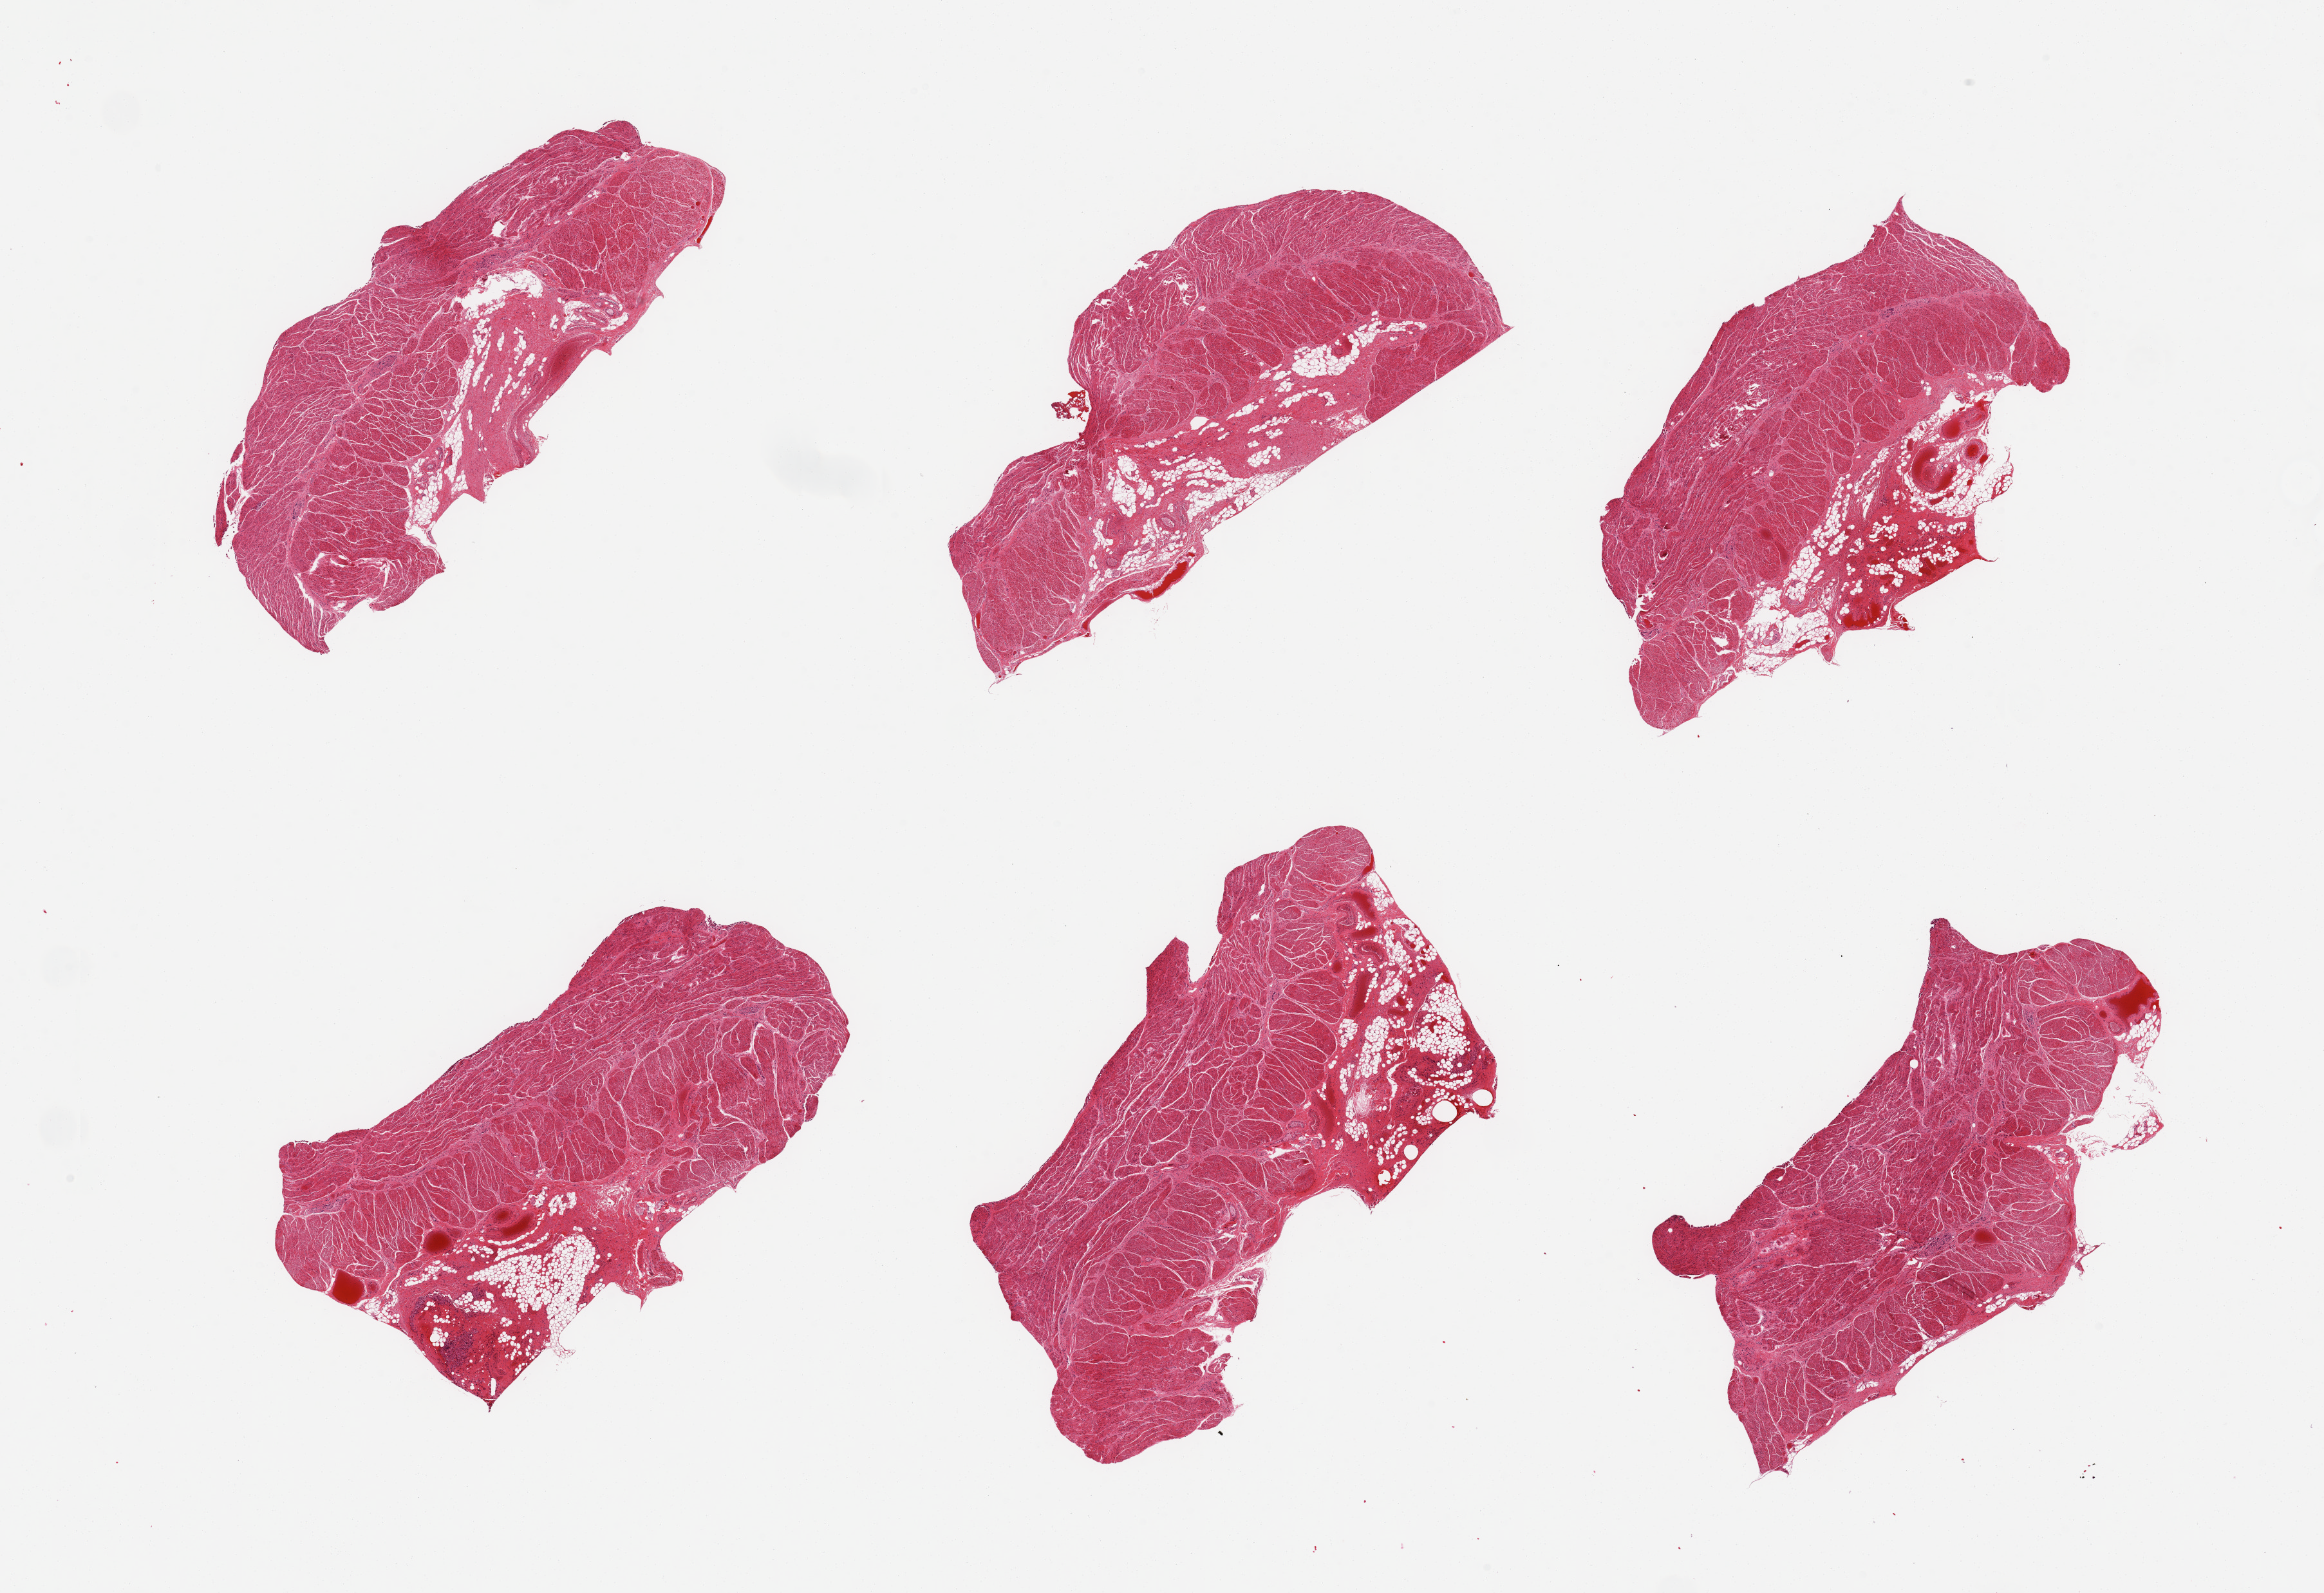
Whole-slide image, hematoxylin and eosin (H&E) stain — low-resolution overview of the scanned area, about 28.5 x 19.6 mm. PAXgene-fixed, paraffin-embedded tissue. Sampled site (target tissue): gastroesophageal junction. Donor tissue sample. Male donor.
* reviewer comment on this tissue sample: 6 pieces; adjacent fat in 4 pieces measures up to 2 mm thick